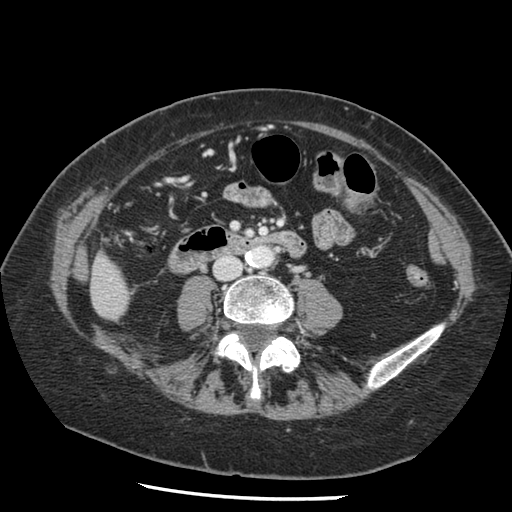
Contrast-enhanced abdominal CT, one axial slice. Reconstruction kernel STANDARD. 120 kVp. Intravenous contrast given. Soft-tissue window (W 400 / L 40 HU). 2.5 mm slice thickness. 512 × 512 image matrix. Female patient, age 85 years. Case-level facts recorded for this patient, not image findings: diagnosis: colorectal cancer liver metastases, imaged before liver resection; multiple liver metastases: no.
Annotated regions visible in this slice (expert manual segmentation):
- liver: bounding box (x1, y1, x2, y2) in pixels: (91, 257, 128, 320)
- planned liver remnant (the part of the liver to remain after resection): (91, 257, 128, 320)